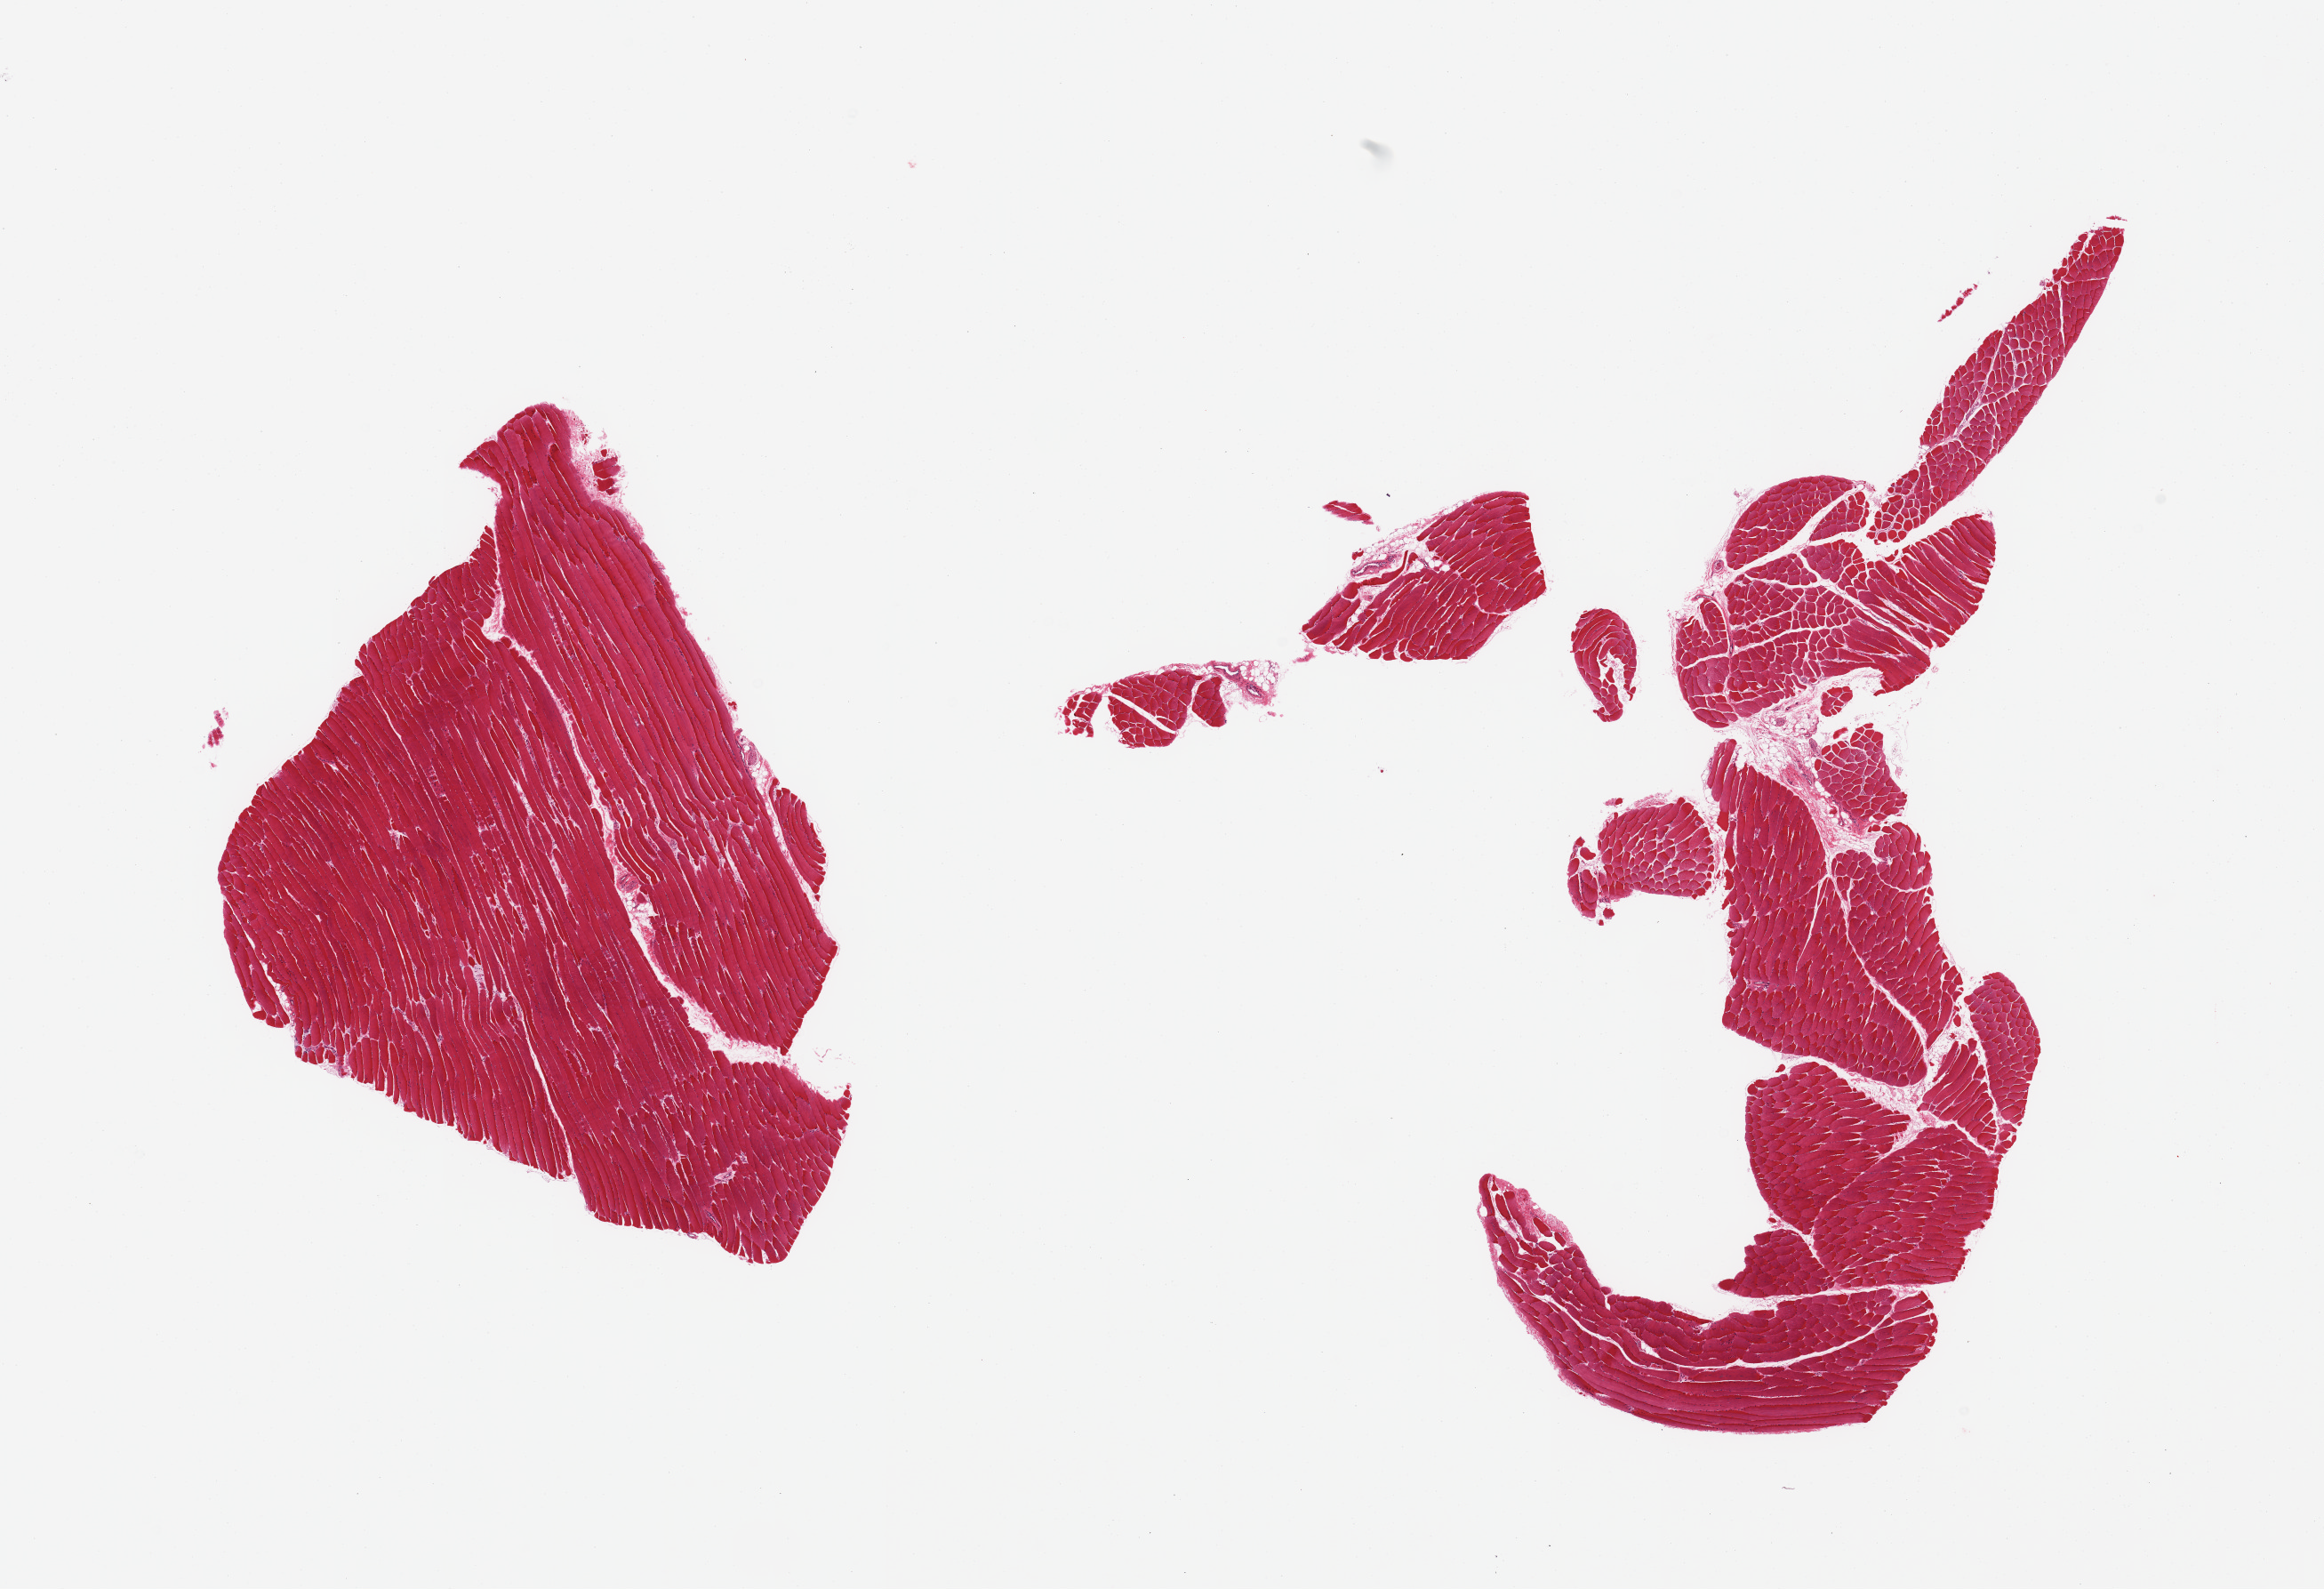
H&E whole-slide image, brightfield — low-resolution overview of the scanned area, about 20.7 x 14.1 mm, PAXgene-fixed, paraffin-embedded tissue, sampled site (target tissue): skeletal muscle, donor tissue sample. Donor: female.
• pathologist's review note for this sample: 2 pieces; one is fragmented